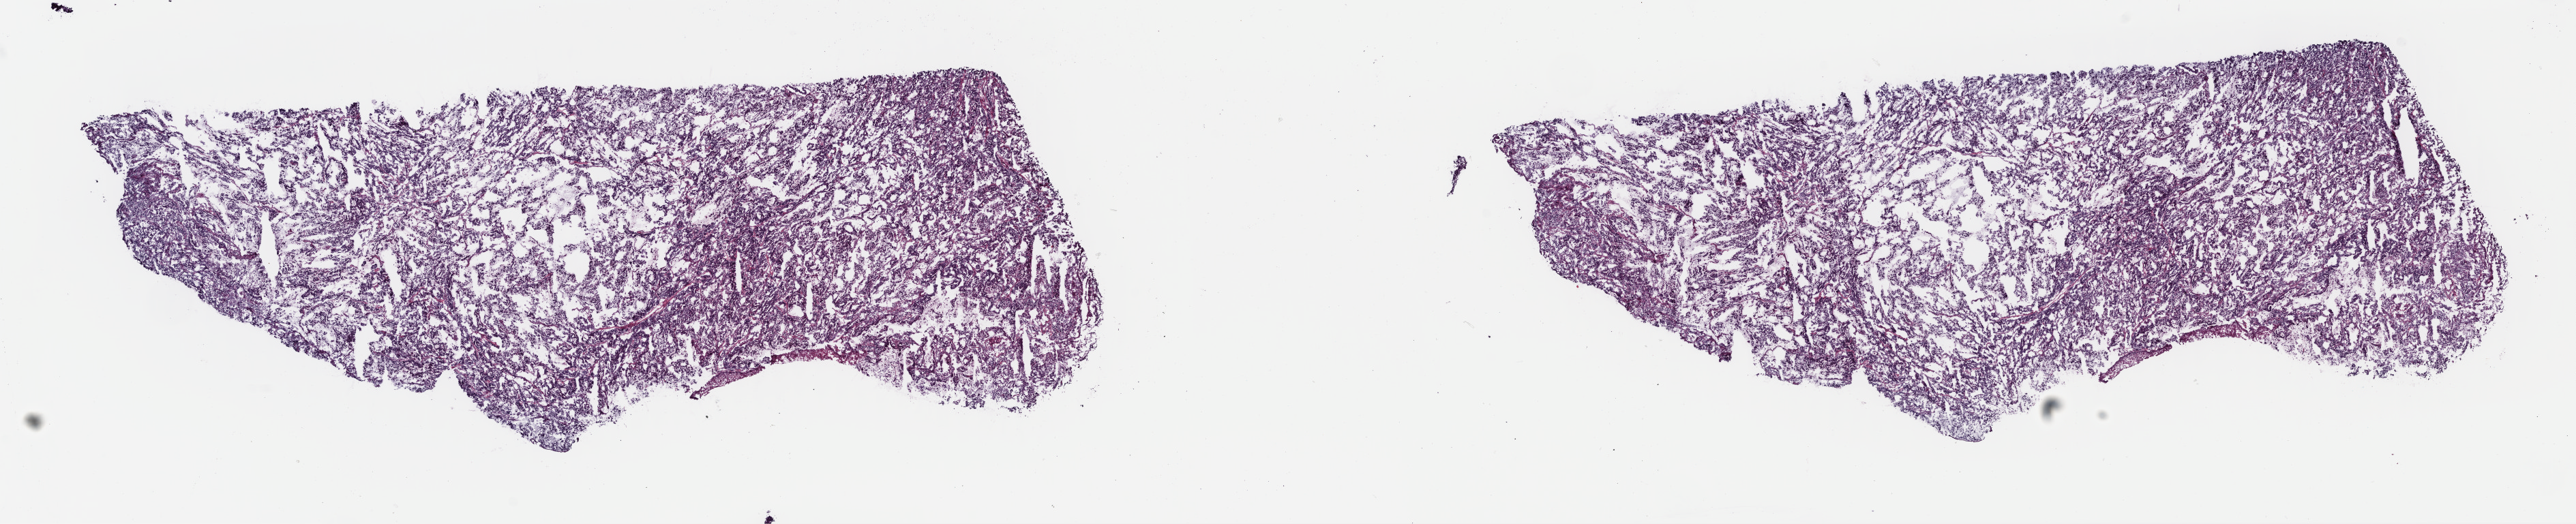
Whole-slide histology image, H&E, whole scanned area (about 29.7 x 6.0 mm, slide scanned at 40x) shown as a low-resolution overview. Frozen section. Primary tumour sample from the esophagus. Male patient; age at initial diagnosis 71 years. Histologic grade: G3 (poorly differentiated). Slide review estimates, as recorded: tumour cells 100%, tumour nuclei 92%, normal cells 0%, stromal cells 0%, necrosis 0%. Infiltration values recorded for this section: lymphocyte infiltration 0%, monocyte infiltration 0%, neutrophil infiltration 0%.
AJCC pathologic stage: IIIB (7th edition). Histologic diagnosis: Adenocarcinoma, NOS (thoracic esophagus). Lymph nodes positive (case pathology): 6 of 6 examined.